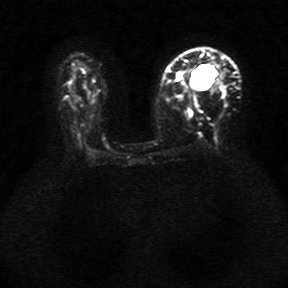
Breast MRI, one axial slice; slice 19 of 34 in the series (ordered by position); diffusion-weighted series; image 2 of 4 stored at this slice position (different b-values; order by instance number); 1.5 T; 5 mm slice thickness; 288 × 288 image matrix, field of view 340 × 340 mm. Female patient.
Outlined on this slice (expert manual segmentation):
- tumour on diffusion-weighted imaging: bounding box [x1, y1, x2, y2] px = [191, 72, 212, 89]